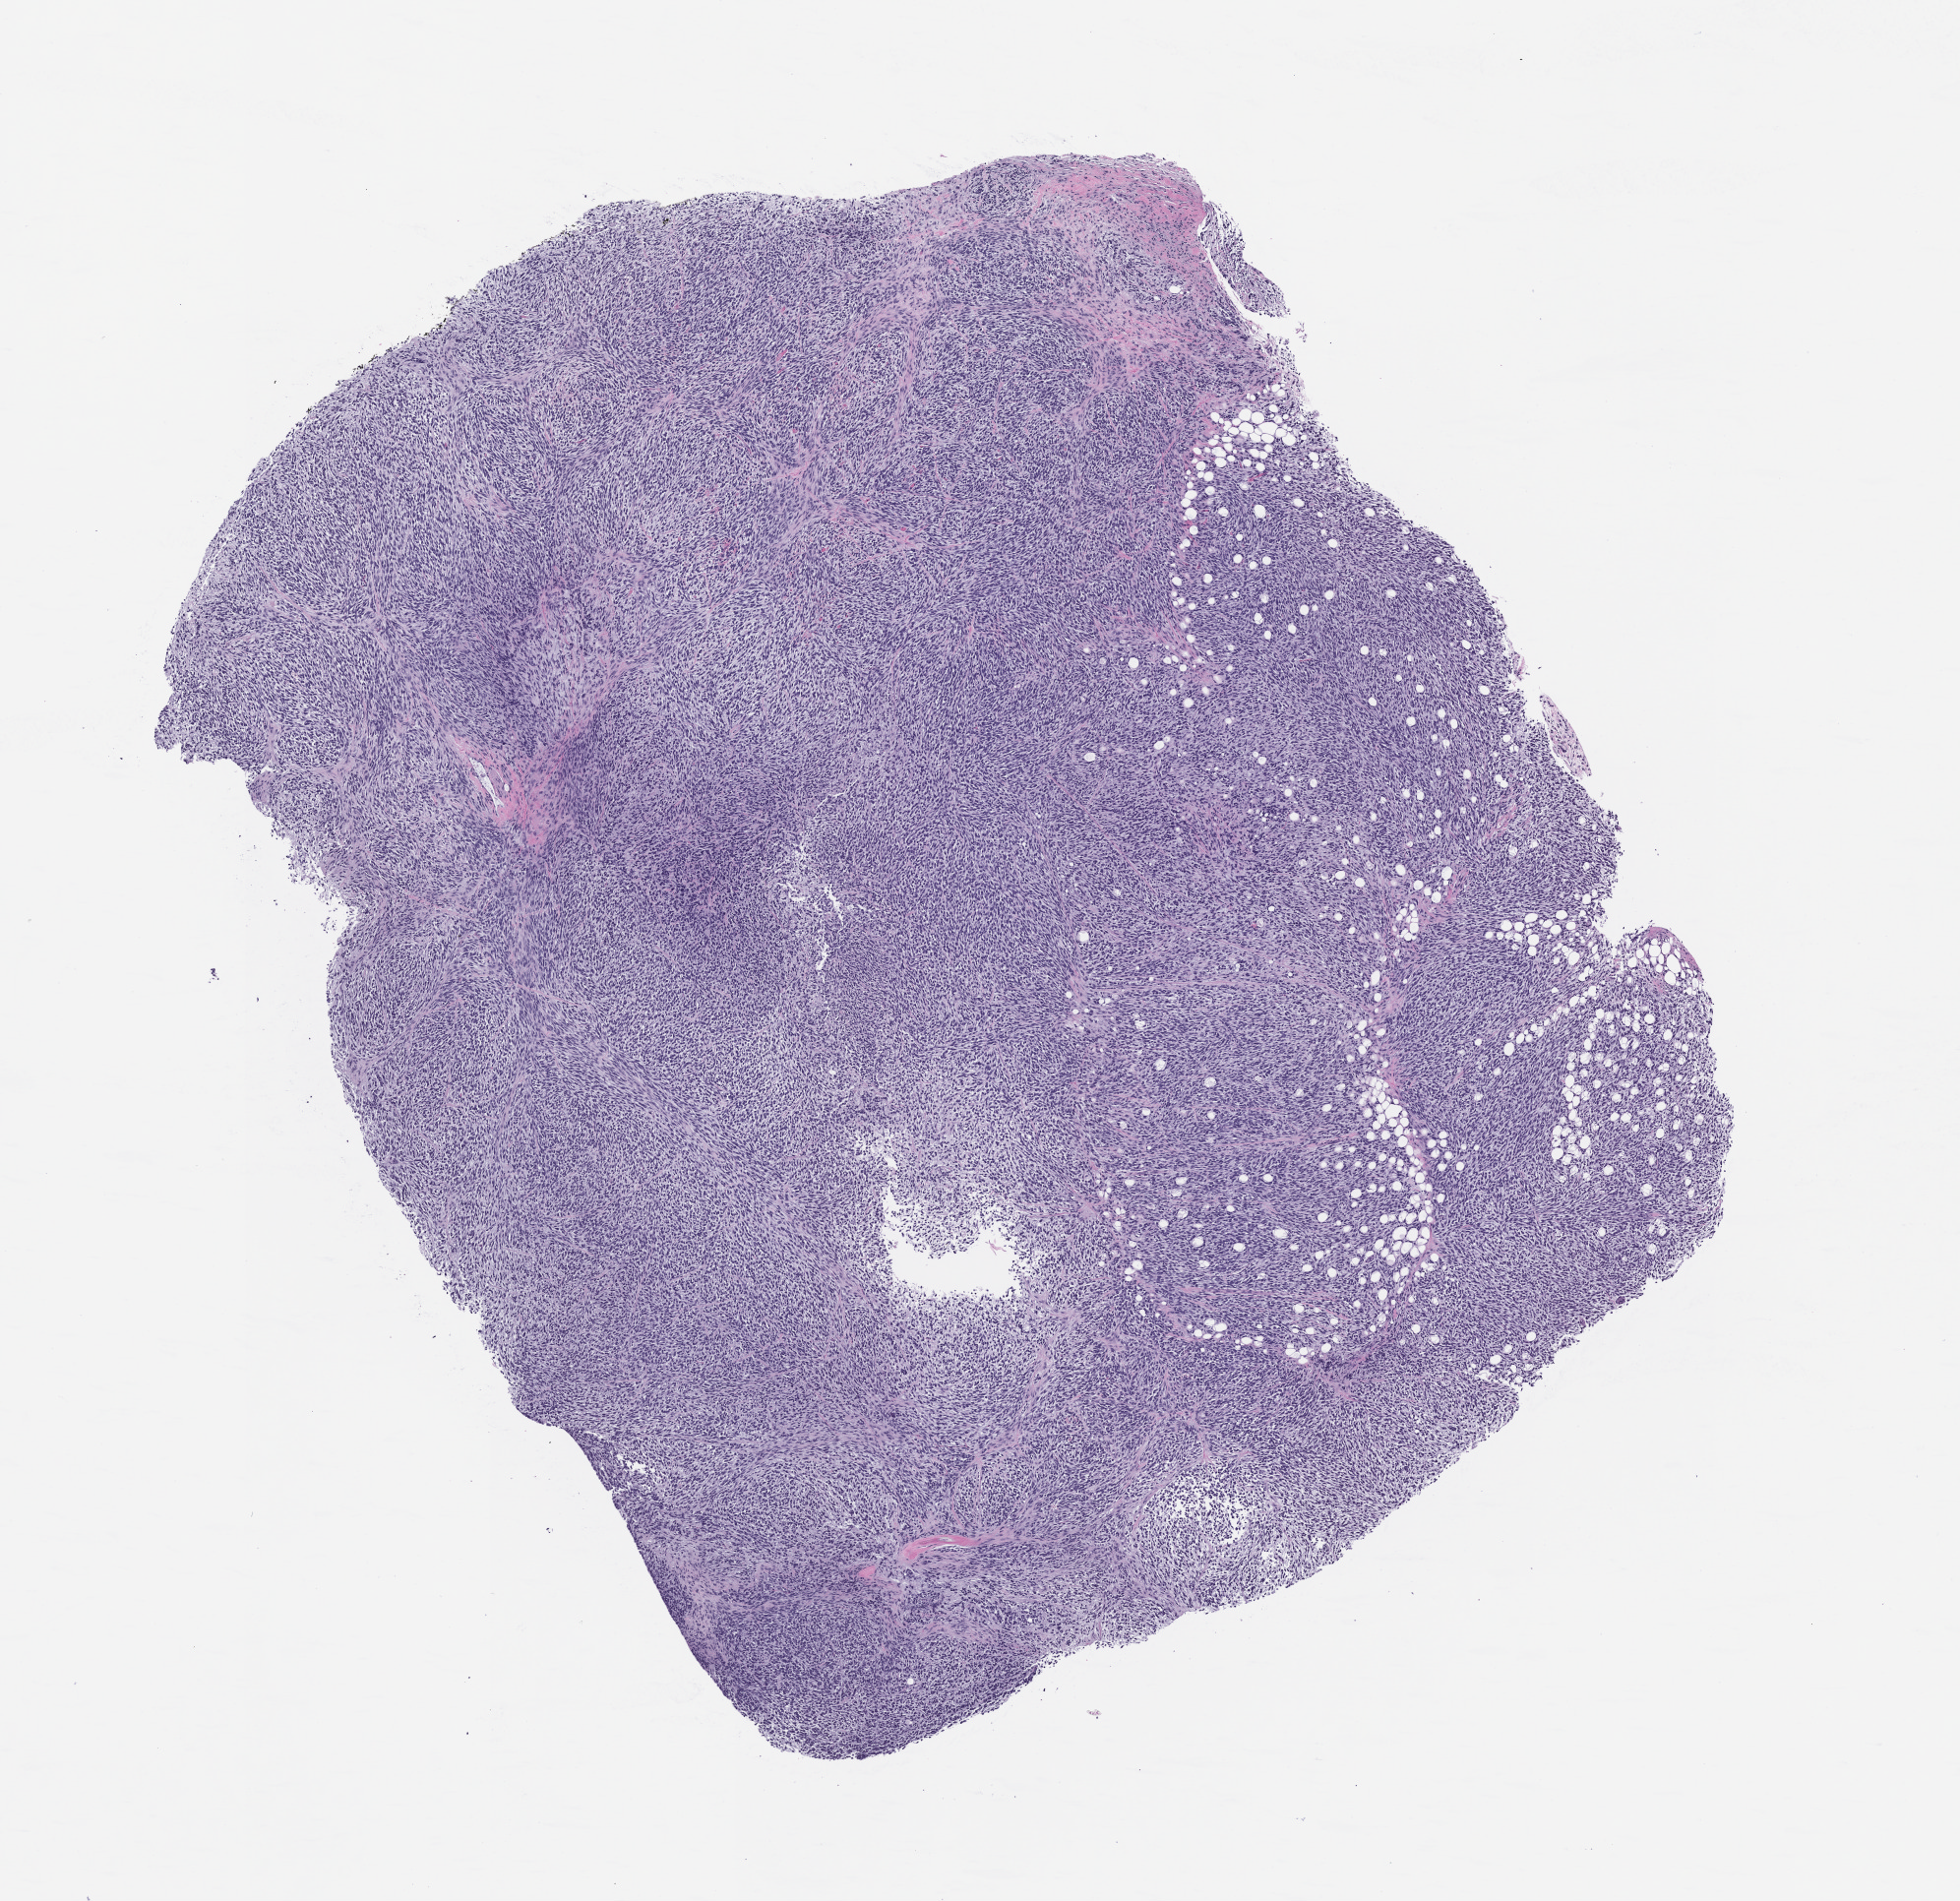
Haematoxylin and eosin whole-slide image of a patient-derived xenograft (PDX) tumor grown in a mouse, passage 3, low-resolution overview of the scanned area, about 8.0 x 7.8 mm; formalin-fixed, paraffin-embedded (FFPE) tissue; originating tumor site category: musculoskeletal.
- originating patient diagnosis: Synovial Sarcoma